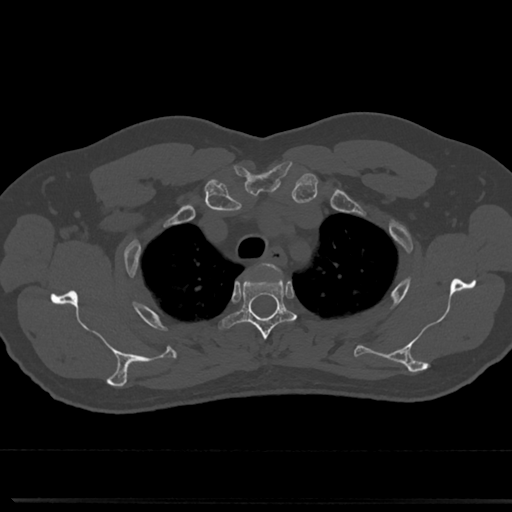
CT including the spine, one axial slice. Position 596 of 817 along the scan axis. Reconstruction kernel Br40s/3. Bone window (W 1800 / L 400 HU). 0.5 mm slice thickness. 512 × 512 image matrix, field of view 355 × 355 mm. Patient: male, 61 years. Case-level facts recorded for this patient, not image findings: primary cancer: prostate.
Annotated regions visible in this slice (semi-automatically segmented with operator editing):
- T3 vertebra: bounding box (x1, y1, x2, y2) in pixels: (228, 267, 294, 346)